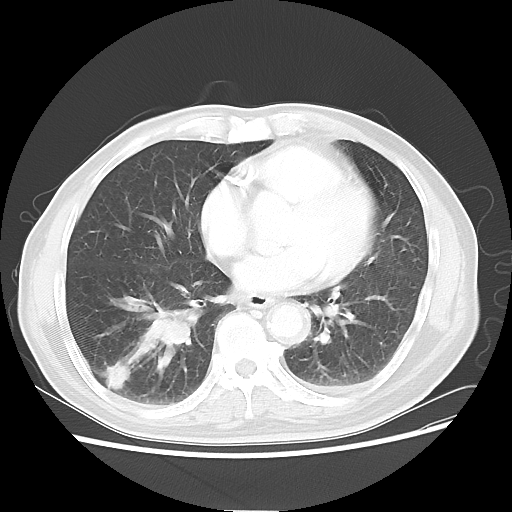
Chest CT, one axial slice. Position 25 of 58 along the scan axis. Reconstruction kernel LUNG. Lung window (W 1500 / L -600 HU). 5 mm slice thickness. 512 × 512 image matrix, field of view 360 × 360 mm. Patient: male, 74 years. From the clinical record (not read from this slice): clinical TNM (as recorded): T1c N1 M1.
Annotated regions visible in this slice (rectangle marked by the reading radiologist):
- lung tumour (recorded histology: adenocarcinoma): bounding box [x1, y1, x2, y2] px = [128, 285, 204, 368]